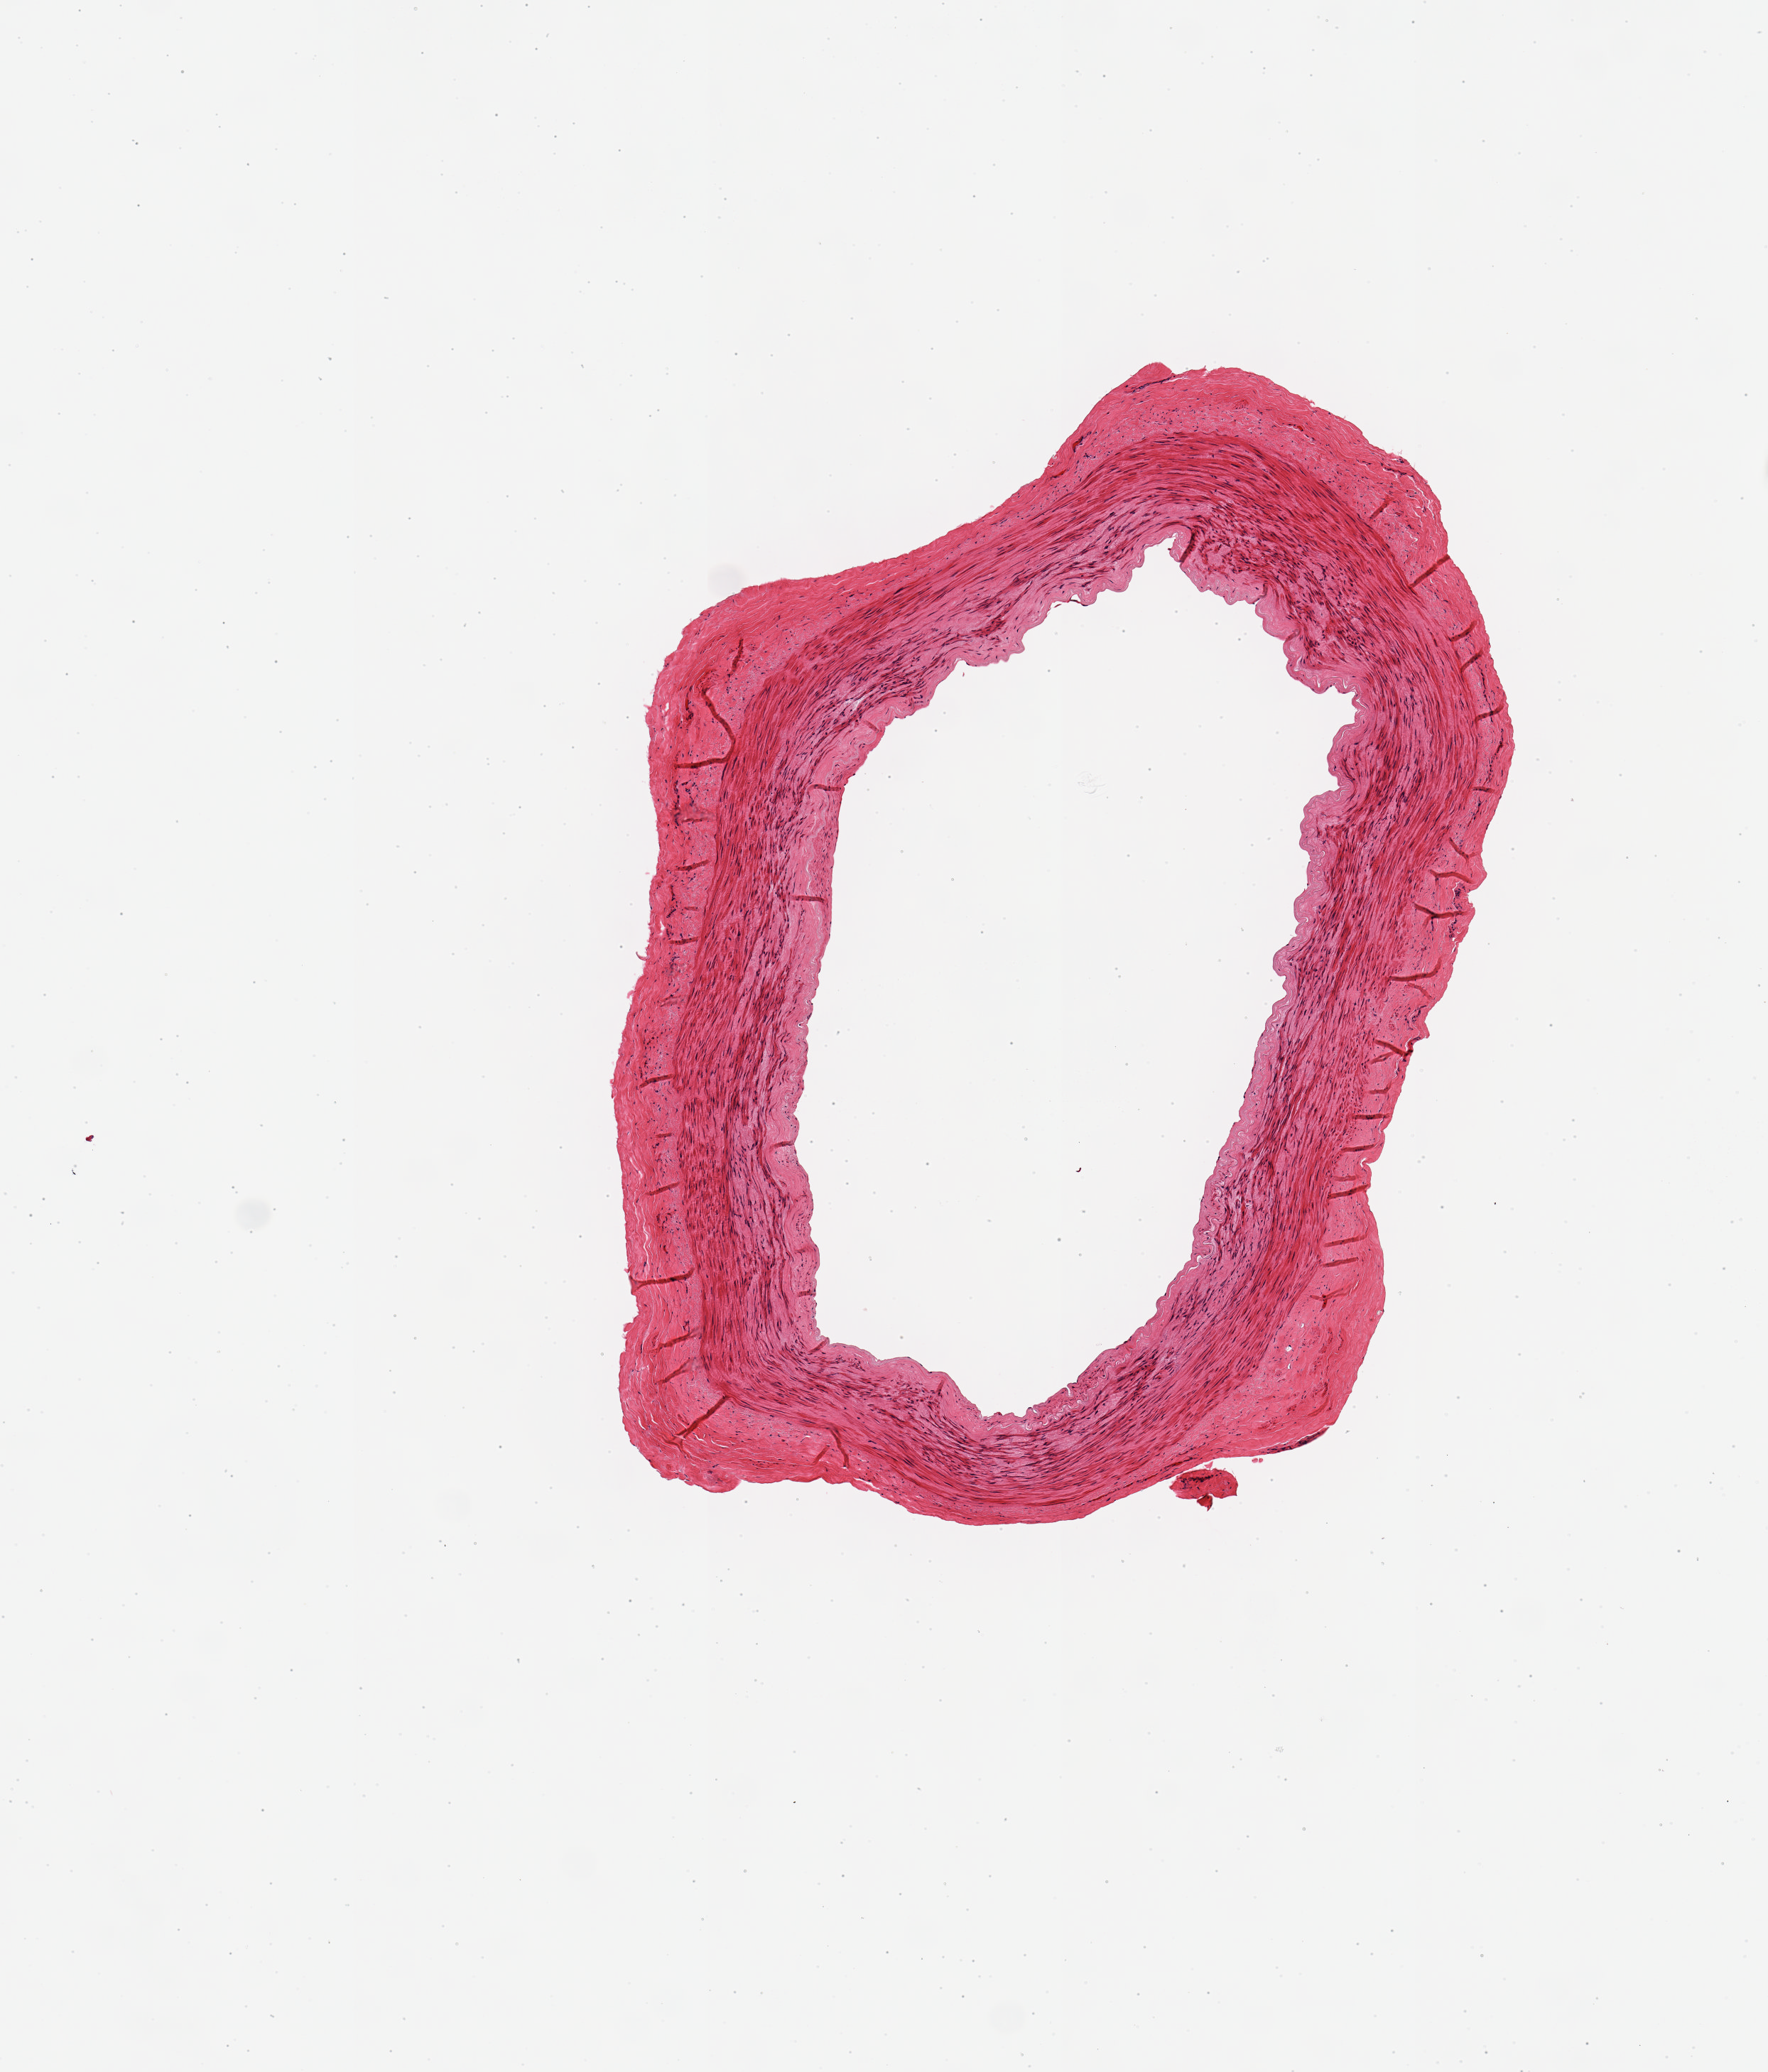
Whole-slide image, haematoxylin and eosin stain — shown as a low-resolution overview of the whole scanned area (about 4.9 x 5.8 mm, acquisition: 20x scan). PAXgene-fixed, paraffin-embedded tissue. Section of tibial artery (target tissue). Tissue donor sample. Donor: male.
Review note (as recorded): 1 piece; artery NOT nerve; no plaque; well trimmed.